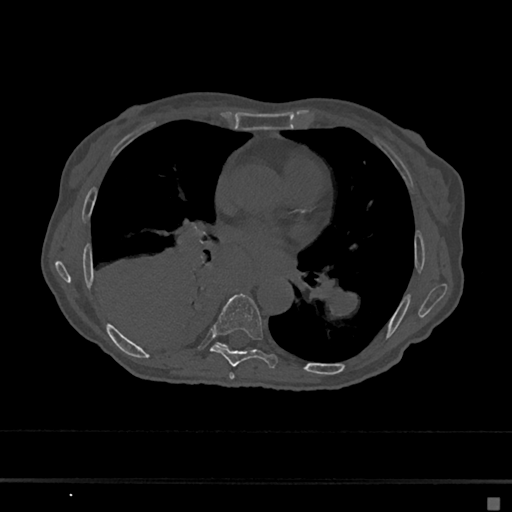
CT including the spine, one axial slice. Position 366 of 797 along the scan axis. Reconstruction kernel Br40s/3. 120 kVp. Bone window (W 1800 / L 400 HU). 0.5 mm slice thickness. 512 × 512 image matrix, field of view 360 × 360 mm. Female patient, age 68 years. Case-level facts recorded for this patient, not image findings: primary cancer: renal.
Structures marked on this image (semi-automatically segmented with operator editing):
- T6 vertebra: bounding box <229,372,235,379> (left, top, right, bottom; pixels)
- T7 vertebra: <210,293,278,369>
- T8 vertebra: <219,344,226,347>